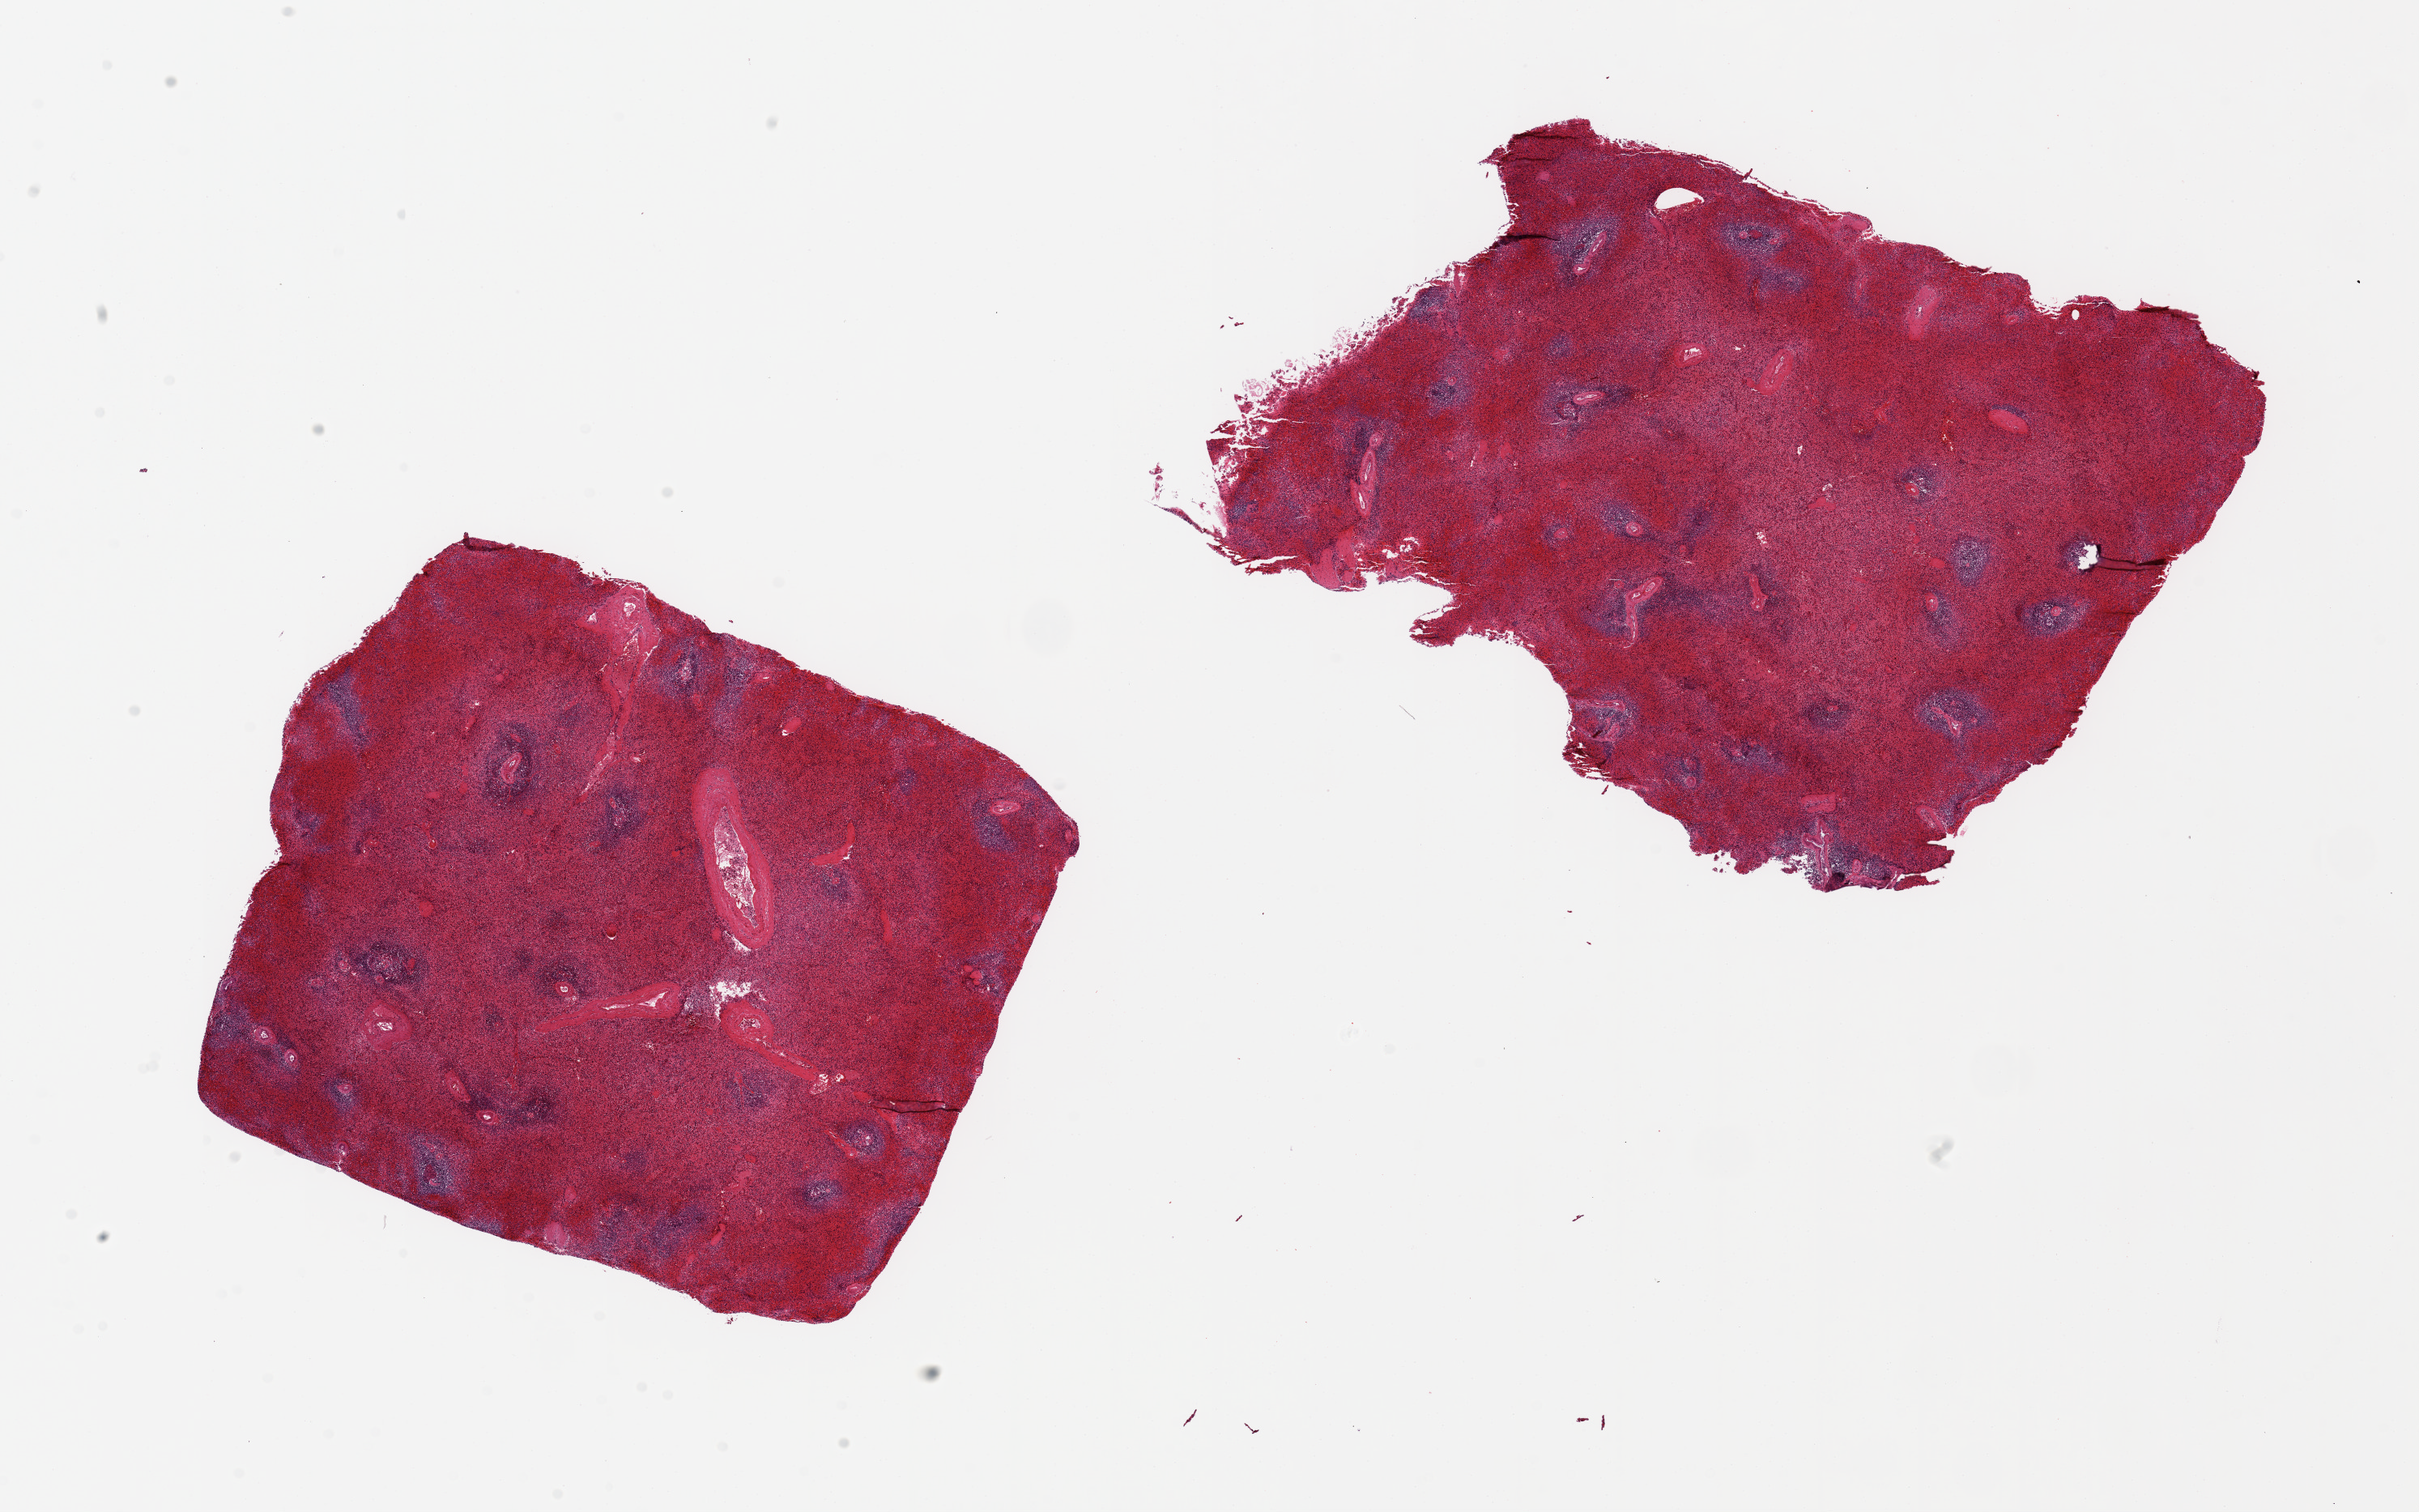
Hematoxylin and eosin (H&E) whole-slide image — whole scanned area (about 23.6 x 14.8 mm, from a 20x scan) shown as a low-resolution overview; PAXgene-fixed, paraffin-embedded tissue; sampled site (target tissue): spleen; donor tissue sample.
Reviewer comment on this tissue sample: 2 pieces ~8x7mm, badly autolyzed, congested.